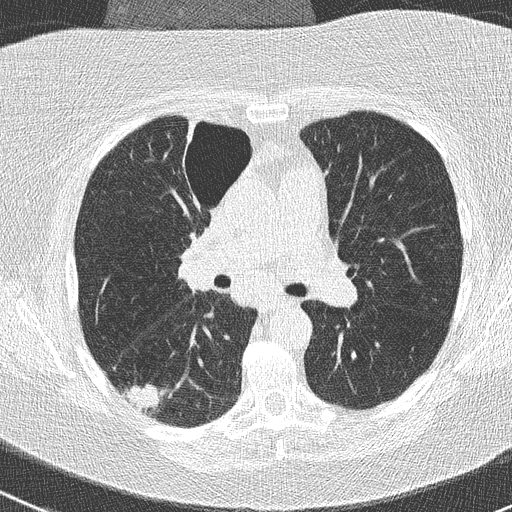
Low-dose screening chest CT, axial slice; first (baseline) screen; lung window (W 1500 / L -600 HU); lung (sharp) reconstruction kernel (B50f); 120 kVp; slice 106 of 261 in the series; 512 × 512 image matrix. Female, age 74 years at enrolment. Former smoker at enrolment.
Expert-annotated lung lesion, bounding box [x1, y1, x2, y2] px = [116, 378, 173, 425]. The screening reader recorded 3 non-calcified nodules or masses ≥4 mm on this exam (right lower lobe, right upper lobe, left lower lobe); which of them this box marks is not recorded. Official screen result: positive, change unspecified: nodule(s) >= 4 mm or enlarging nodule(s), mass(es), or other non-specific abnormalities suspicious for lung cancer. Later outcome: lung cancer diagnosed 16 days after this screen — non-small cell carcinoma, right lower lobe, poorly differentiated (G3), stage IIIA (AJCC 6th edition), 28 mm at pathology.